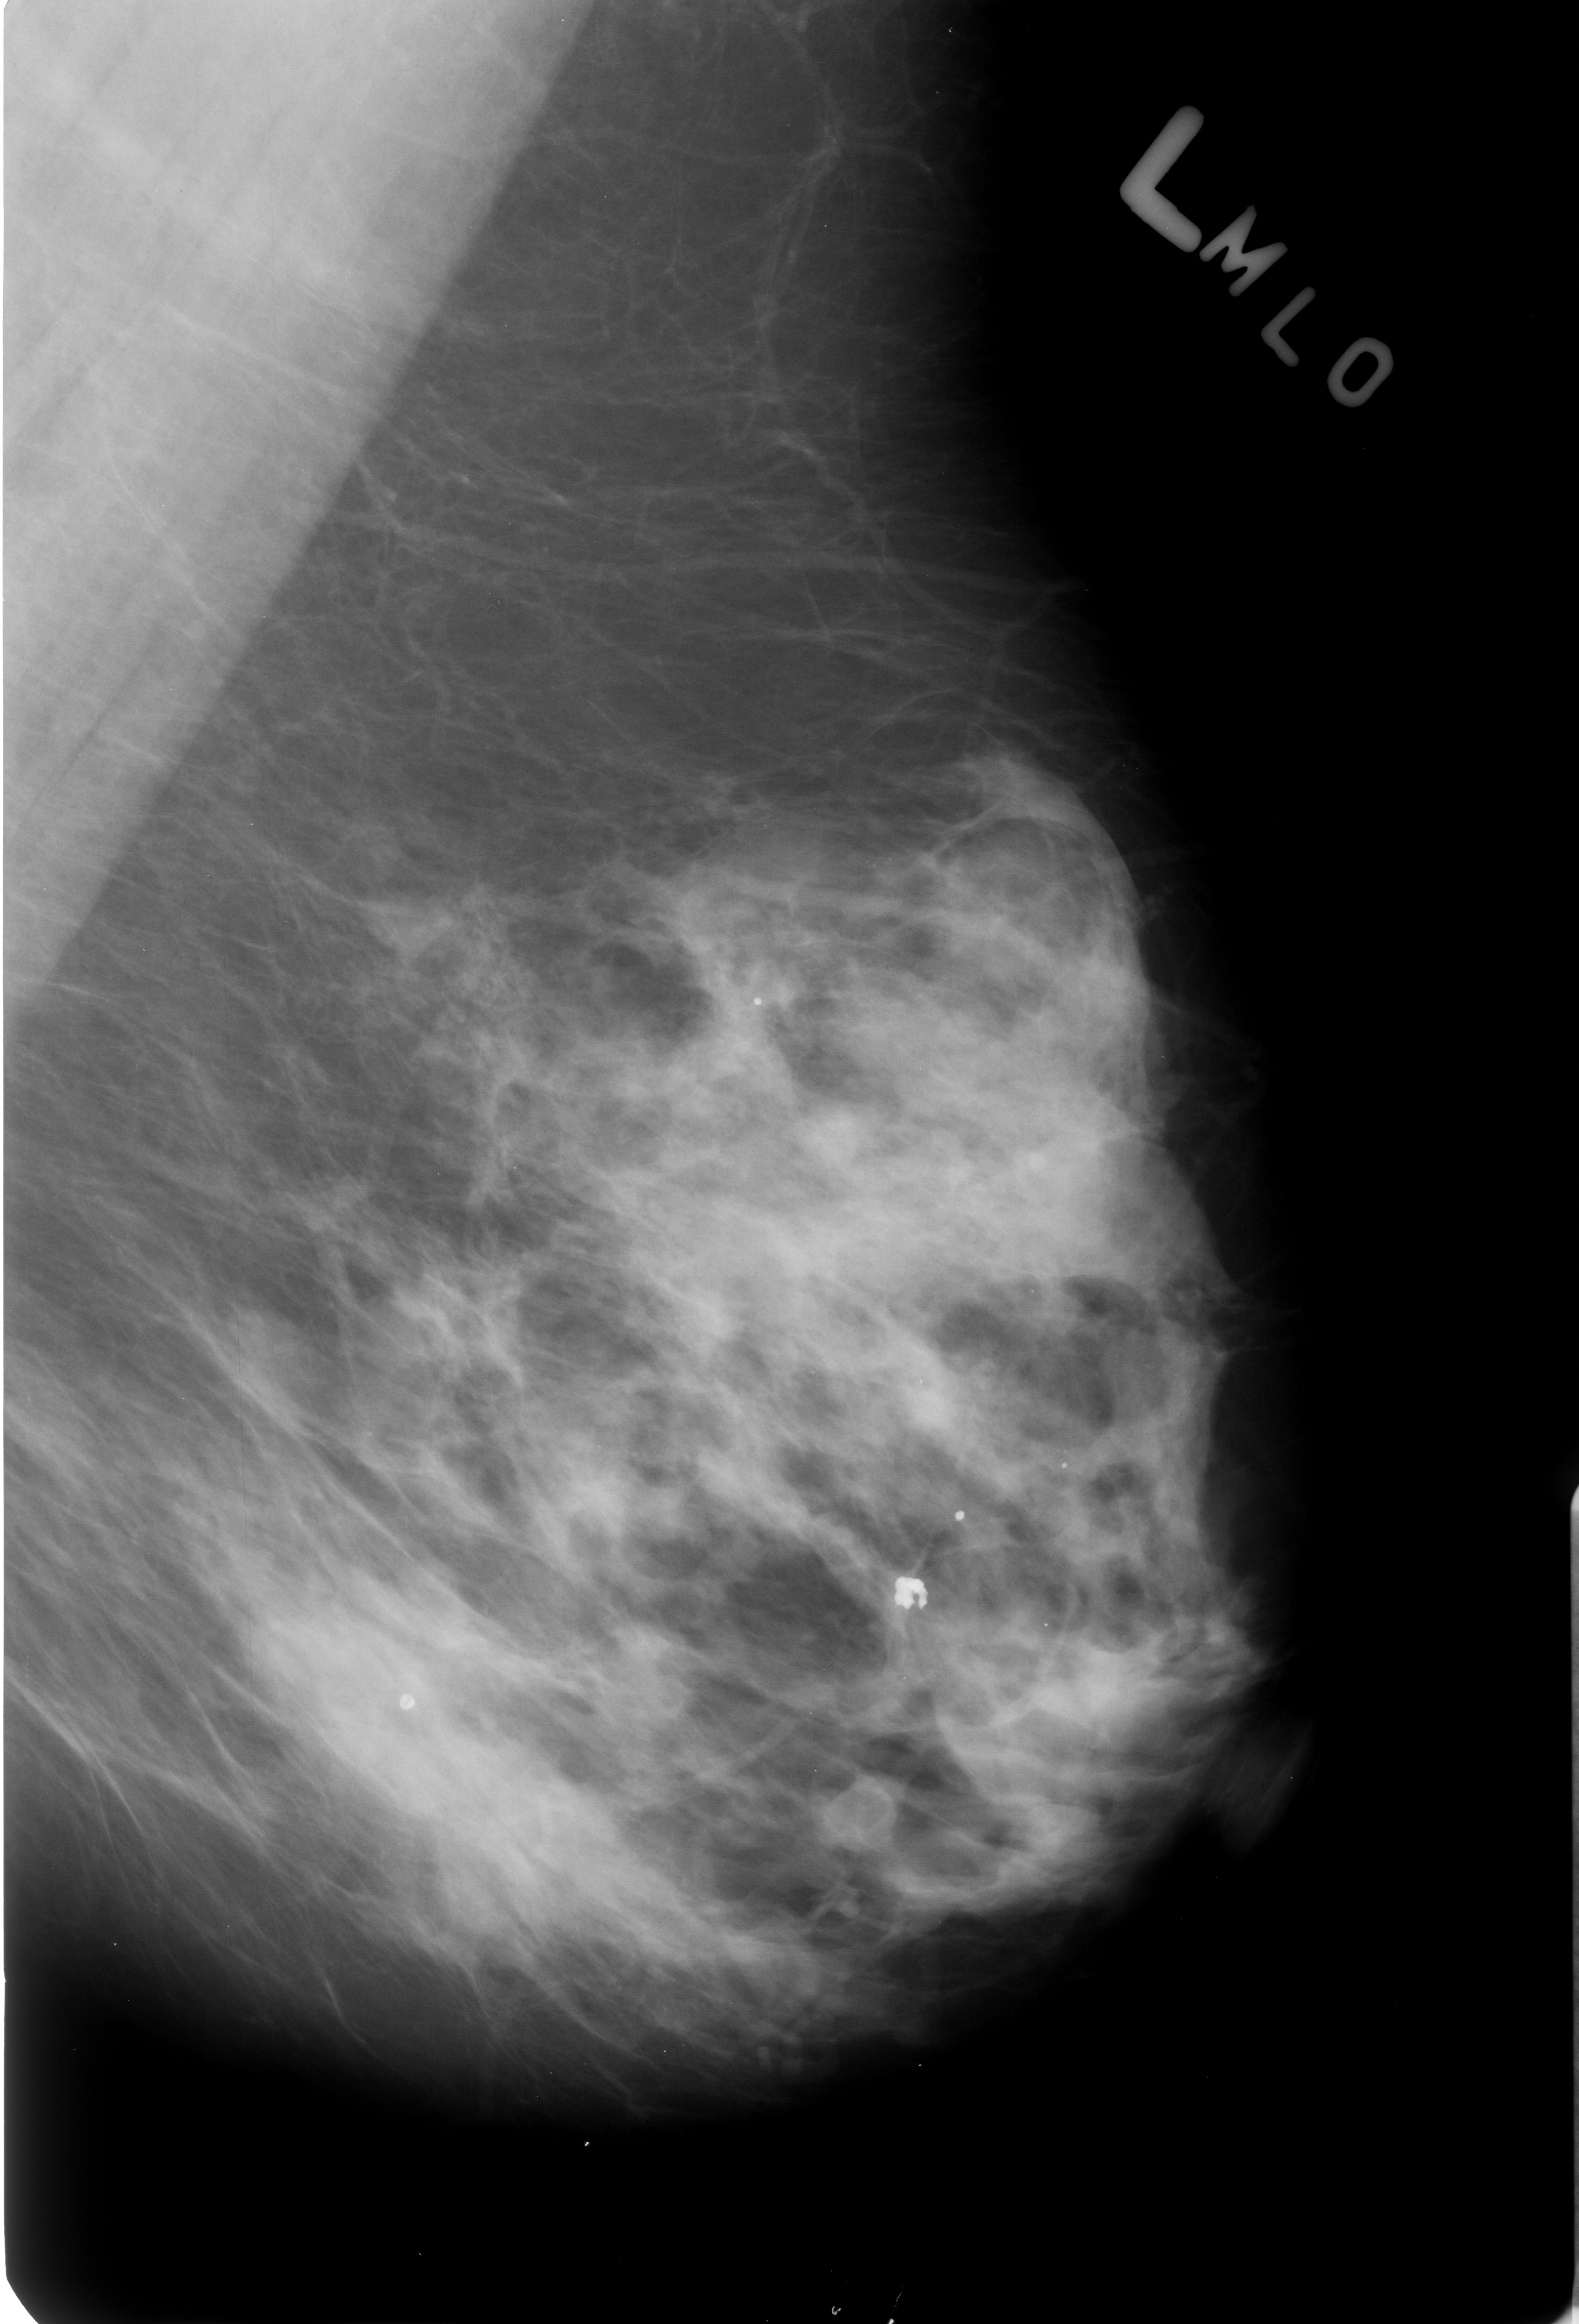
Scanned film-screen mammogram. Left breast. MLO view. BI-RADS breast density category 3 (scale 1–4). 1579 × 2324 image matrix.
Expert-marked regions of interest on this image (one box per marked abnormality):
- calcifications, morphology round and regular / lucent center / dystrophic, distribution diffusely scattered; BI-RADS assessment category 2; subtlety rating 4 on a 1 (subtle) to 5 (obvious) scale; outcome (as recorded, no biopsy): benign without callback (not worked up further): bounding box <882,1570,932,1616> (left, top, right, bottom; pixels)